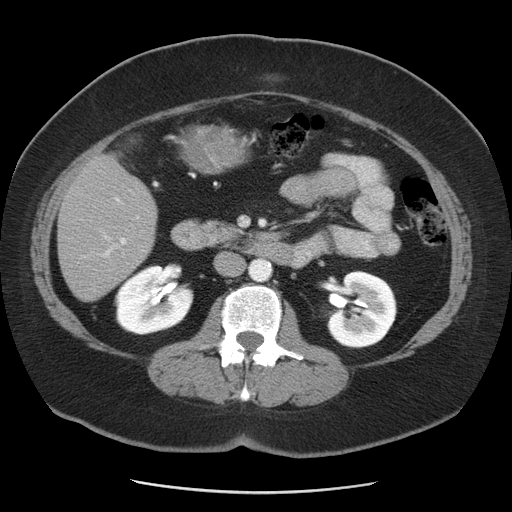
Contrast-enhanced abdominal CT, one axial slice. Position 17 of 55 along the scan axis. 120 kVp. Intravenous contrast given. Soft-tissue window (W 400 / L 40 HU). 5 mm slice thickness. 512 × 512 image matrix. Female patient, age 52 years. Case-level facts recorded for this patient, not image findings: diagnosis: colorectal cancer liver metastases, imaged before liver resection; multiple liver metastases: yes; largest metastasis: 2.5 cm; disease in both lobes: yes.
Structures marked on this image (expert manual segmentation):
- liver: box from (x=59, y=154) to (x=158, y=301) px
- planned liver remnant (the part of the liver to remain after resection): (x=58, y=189)–(x=146, y=301)
- portal vein (with intrahepatic branches): (x=97, y=196)–(x=144, y=258)